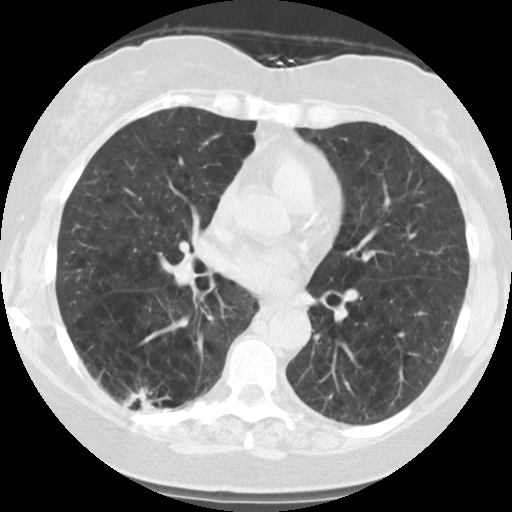
Low-dose screening chest CT, one axial slice; slice 58 of 122 in the series (ordered by position); reconstruction kernel STANDARD; 140 kVp; lung window (W 1500 / L -600 HU); 2.5 mm slice thickness; 512 × 512 image matrix, field of view 310 × 310 mm.
Annotated regions visible in this slice (manually delineated by an expert):
- lesion 1 (tumor, lower lobe of right lung): box from (x=123, y=387) to (x=160, y=411) px